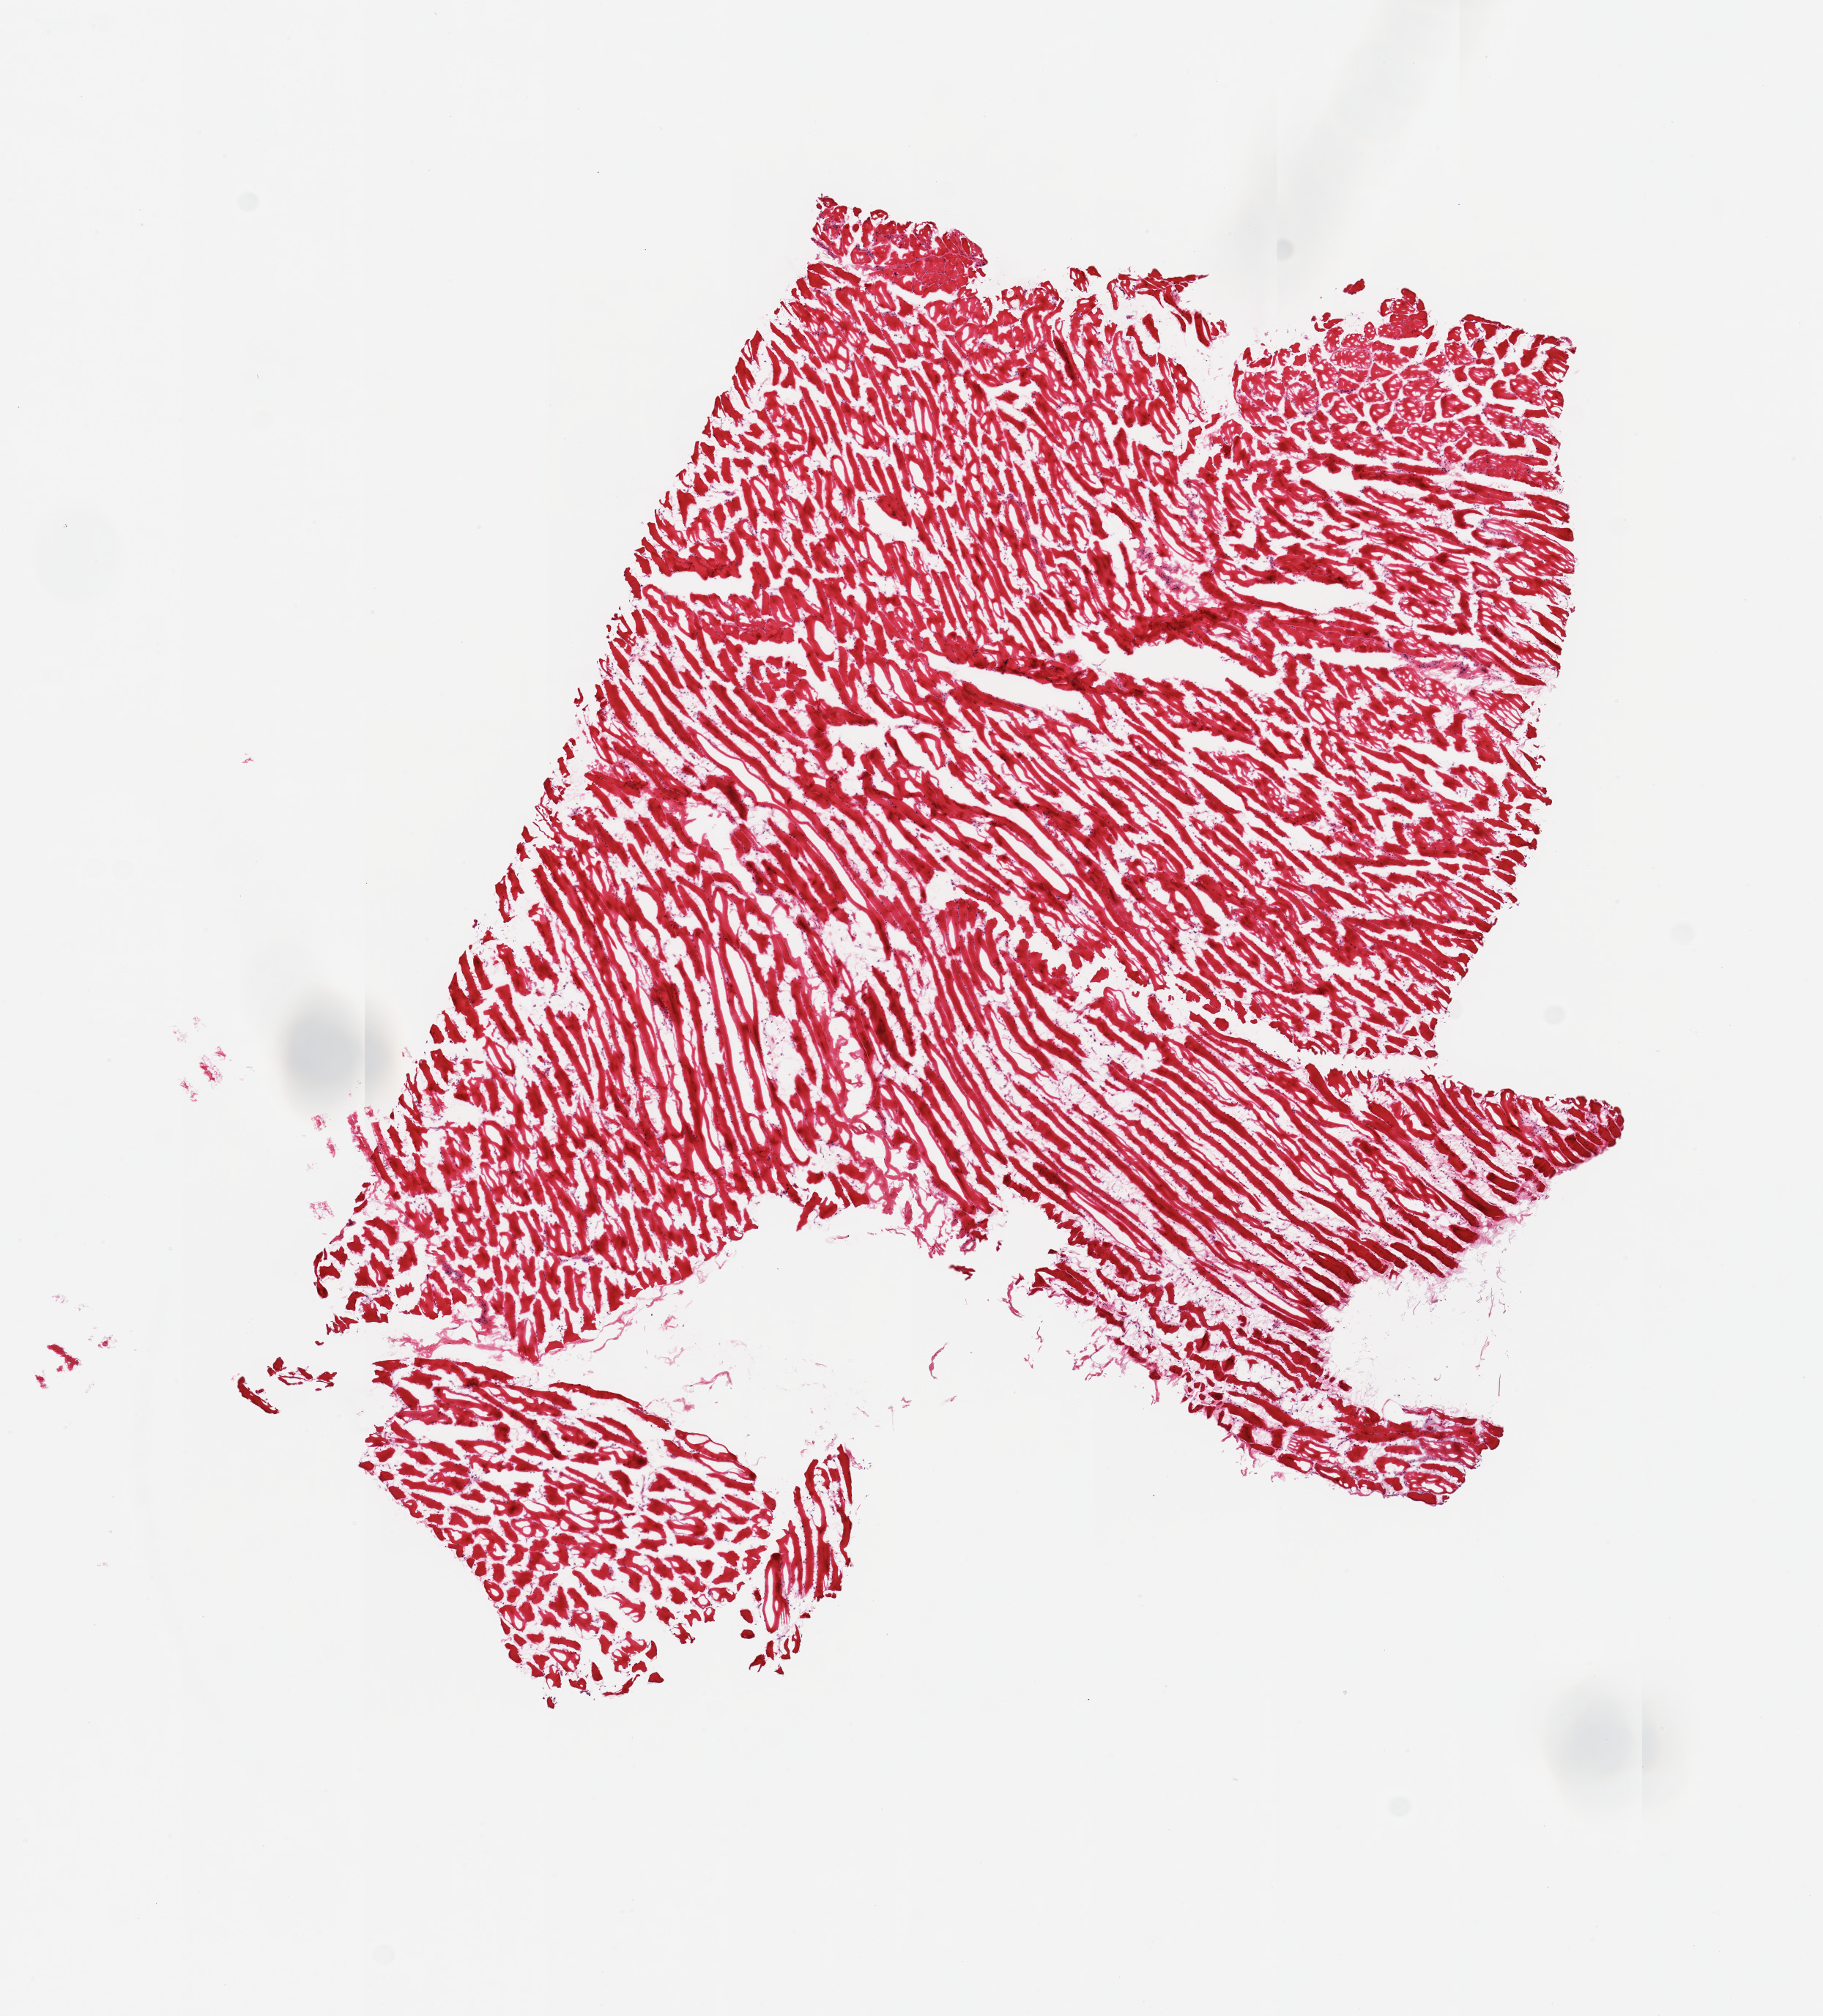
Haematoxylin and eosin whole-slide image — low-resolution overview of the scanned area, about 9.8 x 10.9 mm (slide scanned at 20x). Frozen section (dry ice). Section of skeletal muscle (target tissue). Tissue donor sample. Male donor.
- review note (as recorded): 1 piece